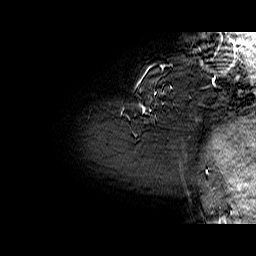
Breast MRI (dynamic contrast-enhanced), one sagittal slice; position 56 of 60 along the scan axis; dynamic contrast-enhanced series, time point 2 of 6 at this slice position (early post-contrast); 1.5 T; TE 6.4 ms, TR 32.9 ms; 256 × 256 image matrix, field of view 200 × 200 mm. Female patient. From the clinical record (not read from this slice): setting: breast cancer imaged before/during neoadjuvant chemotherapy; receptor status: HER2-positive.
Outlined on this slice (semi-automatically segmented with operator editing):
- analysis volume of interest (the breast-tissue region the enhancement analysis was run in; not a lesion): bounding box [x1, y1, x2, y2] px = [130, 62, 210, 128]
- tumour enhancement mask (voxels above the 100 % enhancement threshold inside the analysis volume of interest): [149, 66, 151, 68]